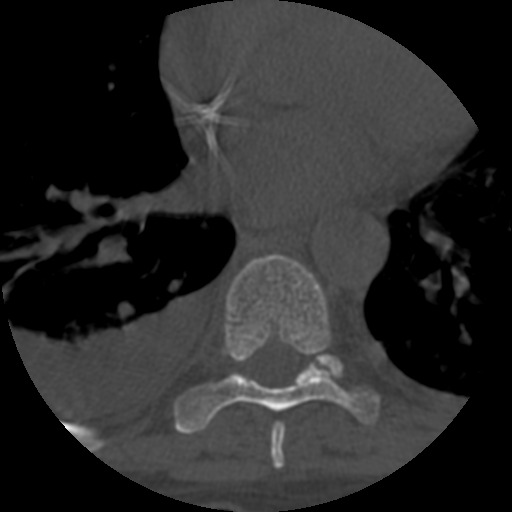
CT including the spine, one axial slice. Slice 397 of 708 in the series (ordered by position). 120 kVp. One of 3 acquisitions stored at this slice position. Bone window (W 1800 / L 400 HU). 512 × 512 image matrix, field of view 160 × 160 mm. Patient age 55 years. From the clinical record (not read from this slice): primary cancer: colon.
Structures marked on this image (semi-automatically segmented with operator editing):
- T7 vertebra: bounding box <270,423,285,467> (left, top, right, bottom; pixels)
- T8 vertebra: <174,254,379,434>
- T9 vertebra: <316,354,344,377>